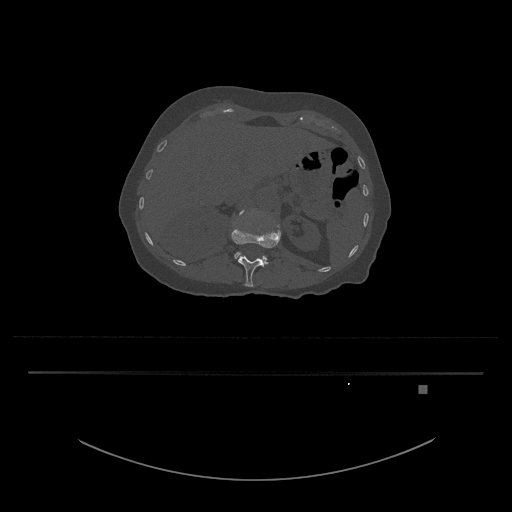
CT including the spine, one axial slice; slice 537 of 797 in the series (ordered by position); reconstruction kernel Br40s/3; 120 kVp; bone window (W 1800 / L 400 HU); 0.5 mm slice thickness; 512 × 512 image matrix, field of view 500 × 500 mm. Patient: female, 57 years. From the clinical record (not read from this slice): primary cancer: cervical.
Structures marked on this image (semi-automatic segmentation, software-assisted and operator-edited):
- L1 vertebra: bounding box (x1, y1, x2, y2) in pixels: (231, 222, 281, 287)